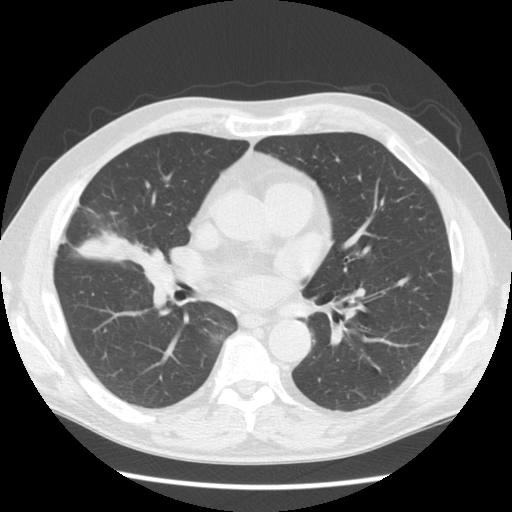
Low-dose screening chest CT, one axial slice; position 78 of 146 along the scan axis; reconstruction kernel STANDARD; 120 kVp; lung window (W 1500 / L -600 HU); 512 × 512 image matrix, field of view 350 × 350 mm.
Outlined on this slice (outlined manually by an expert reader):
- lesion 1 (tumor, middle lobe of right lung): bounding box [x1, y1, x2, y2] px = [81, 239, 112, 256]